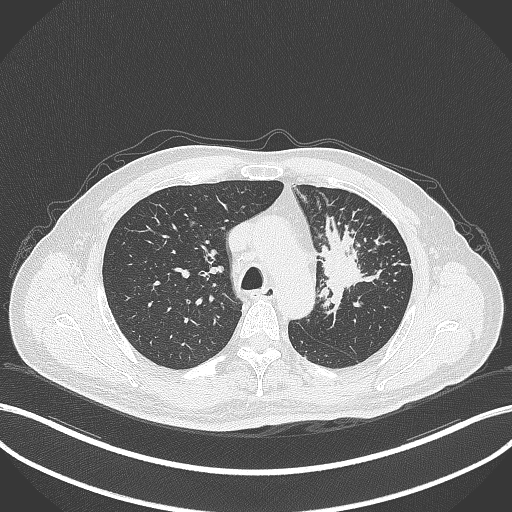
Chest CT, one axial slice; position 251 of 386 along the scan axis; 120 kVp; lung window (W 1500 / L -600 HU); 1 mm slice thickness; 512 × 512 image matrix, field of view 400 × 400 mm. Male patient, age 69 years. Case-level facts recorded for this patient, not image findings: clinical TNM (as recorded): T2a N2 M0; histopathological grade: G2-3.
Annotated regions visible in this slice (rectangle marked by the reading radiologist):
- lung tumour (recorded histology: adenocarcinoma): bounding box <318,221,369,303> (left, top, right, bottom; pixels)